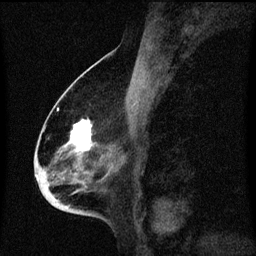
Breast MRI (dynamic contrast-enhanced), one sagittal slice. Position 34 of 60 along the scan axis. Dynamic contrast-enhanced series, image 2 of 3 at this slice position (ordered by acquisition). 1.5 T. TE 4.2 ms, TR 8.4 ms. 2 mm slice thickness. 256 × 256 image matrix. Patient: female, 68 years. Case-level facts recorded for this patient, not image findings: setting: breast cancer imaged before/during neoadjuvant chemotherapy; receptor status: triple-negative.
Outlined on this slice (semi-automatic segmentation, software-assisted and operator-edited):
- analysis volume of interest (the breast-tissue region the enhancement analysis was run in; not a lesion): bounding box [x1, y1, x2, y2] px = [36, 96, 113, 213]
- tumour enhancement mask (voxels above the 70 % enhancement threshold inside the analysis volume of interest): [41, 120, 92, 185]